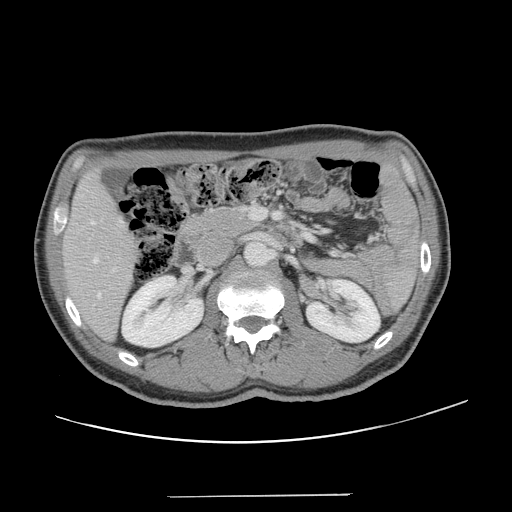
Contrast-enhanced abdominal CT, one axial slice. Position 64 of 131 along the scan axis. 120 kVp. Intravenous contrast given. Soft-tissue window (W 400 / L 40 HU). 512 × 512 image matrix. Male patient, age 60 years. From the clinical record (not read from this slice): diagnosis: colorectal cancer liver metastases, imaged before liver resection.
Outlined on this slice (expert manual segmentation):
- hepatic veins: bounding box [x1, y1, x2, y2] px = [91, 221, 101, 298]
- liver: [64, 174, 135, 338]
- planned liver remnant (the part of the liver to remain after resection): [64, 174, 134, 339]